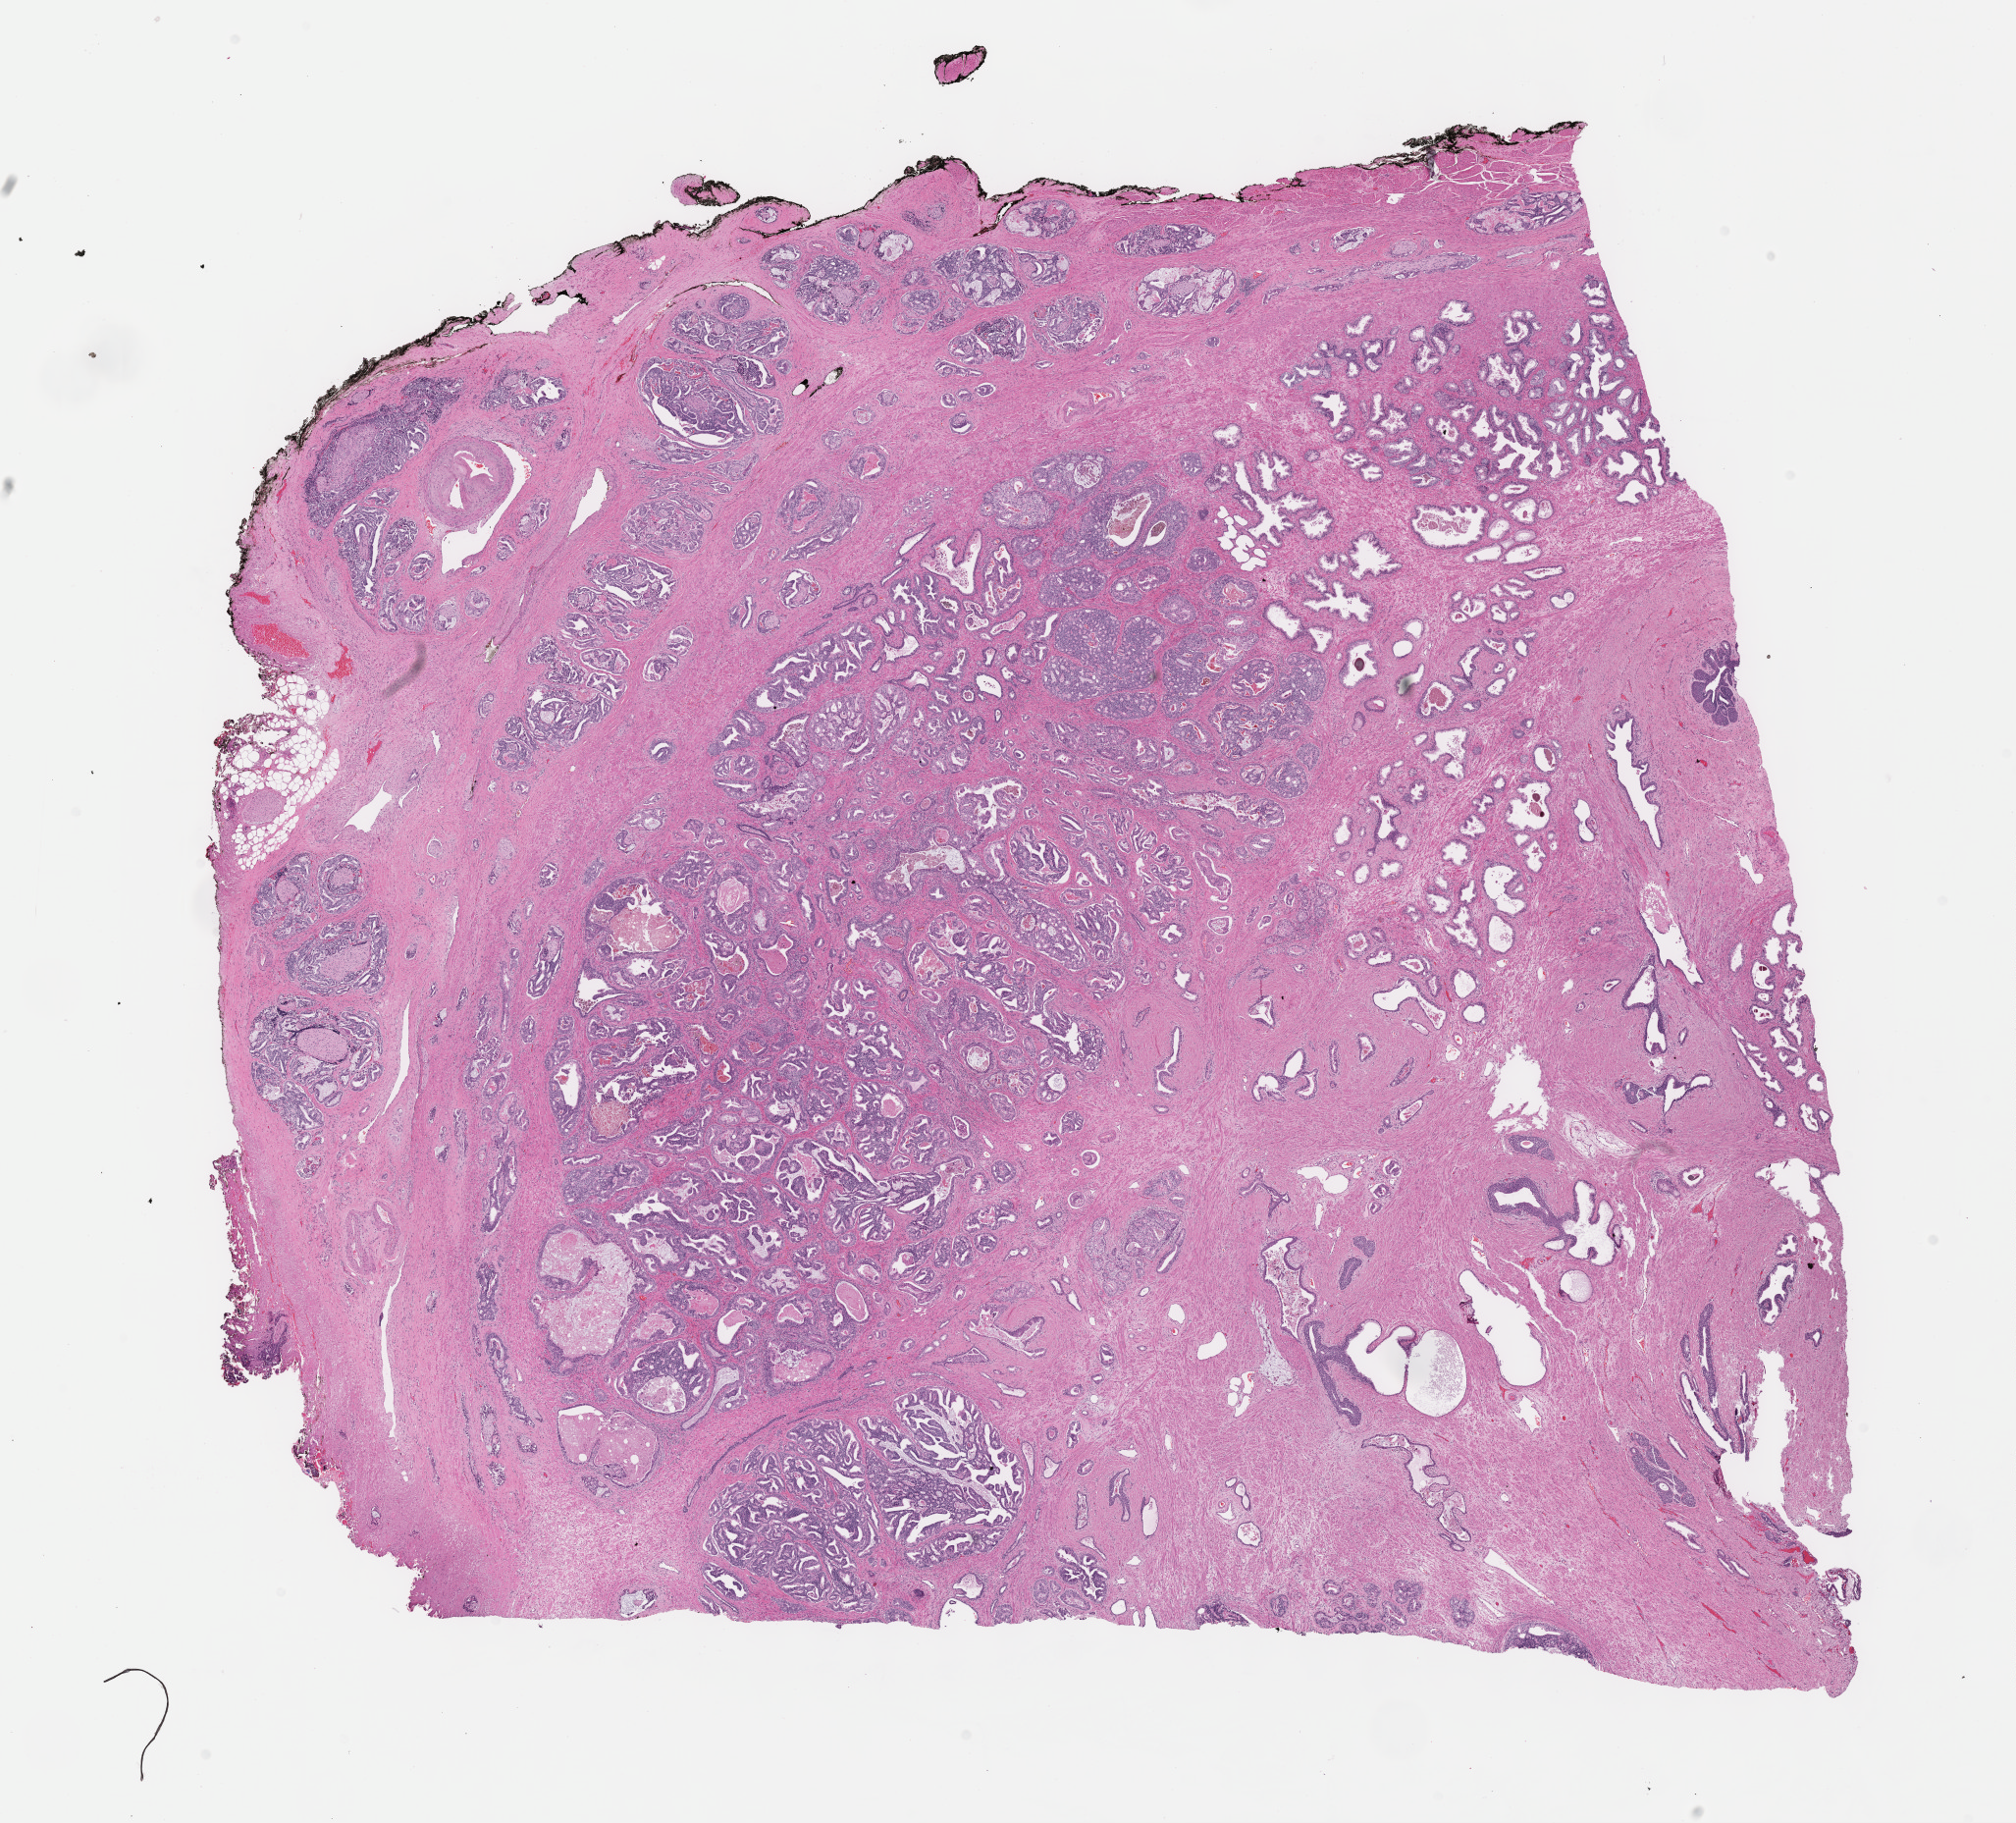
Whole-slide histology image, H&E, shown as a low-resolution overview of the whole scanned area (about 16.6 x 15.0 mm, slide scanned at 40x), FFPE section, sample: primary tumour, prostate. Patient: male, age at initial diagnosis 63 years.
Histologic diagnosis: Adenocarcinoma, NOS (prostate gland).